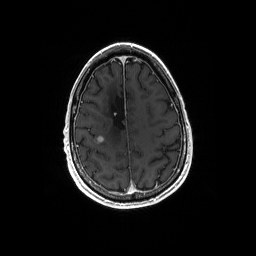
Brain MRI from a brain-tumour surgery series, one axial slice; position 50 of 192 along the scan axis; T1-weighted post-contrast; 1 mm slice thickness; 256 × 256 image matrix, field of view 256 × 256 mm. From the clinical record (not read from this slice): histopathology: Astrocytoma; WHO grade: 4; IDH mutation: yes; tumour location: Right Frontal.
Structures marked on this image (outlined manually by an expert reader):
- tumour: bounding box <95,137,104,144> (left, top, right, bottom; pixels)